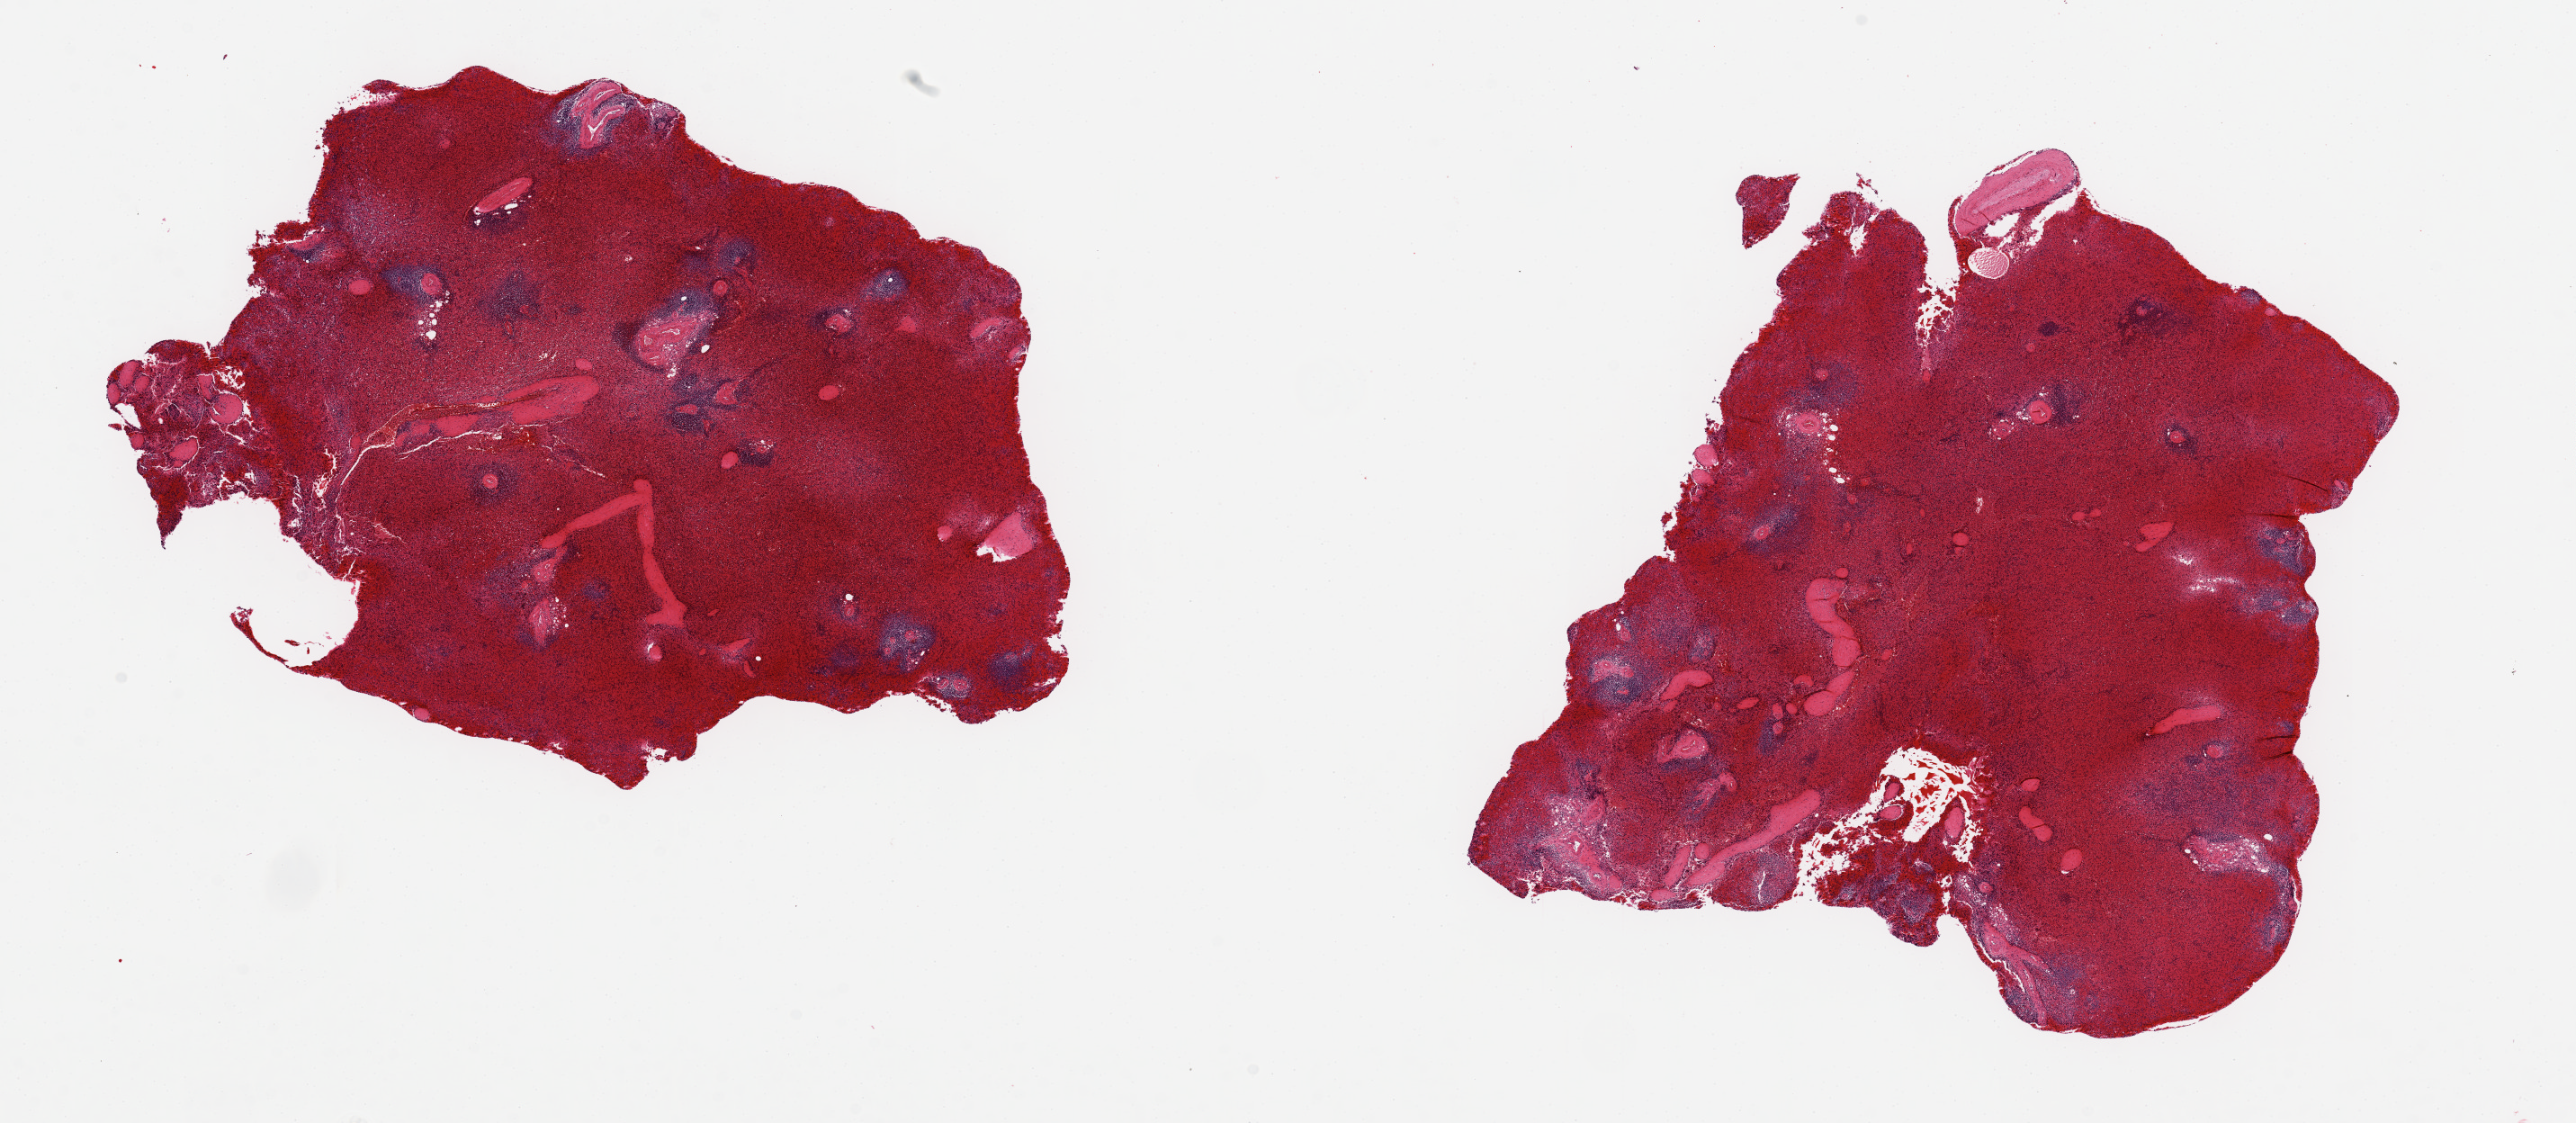
Digitized hematoxylin and eosin (H&E)-stained section, brightfield — whole scanned area (about 22.6 x 9.9 mm) shown as a low-resolution overview, PAXgene-fixed, paraffin-embedded tissue, section of spleen (target tissue), donor tissue sample. Donor: male.
* review note (as recorded): 2 pieces 8x5 & 7x6 mm; severely congested